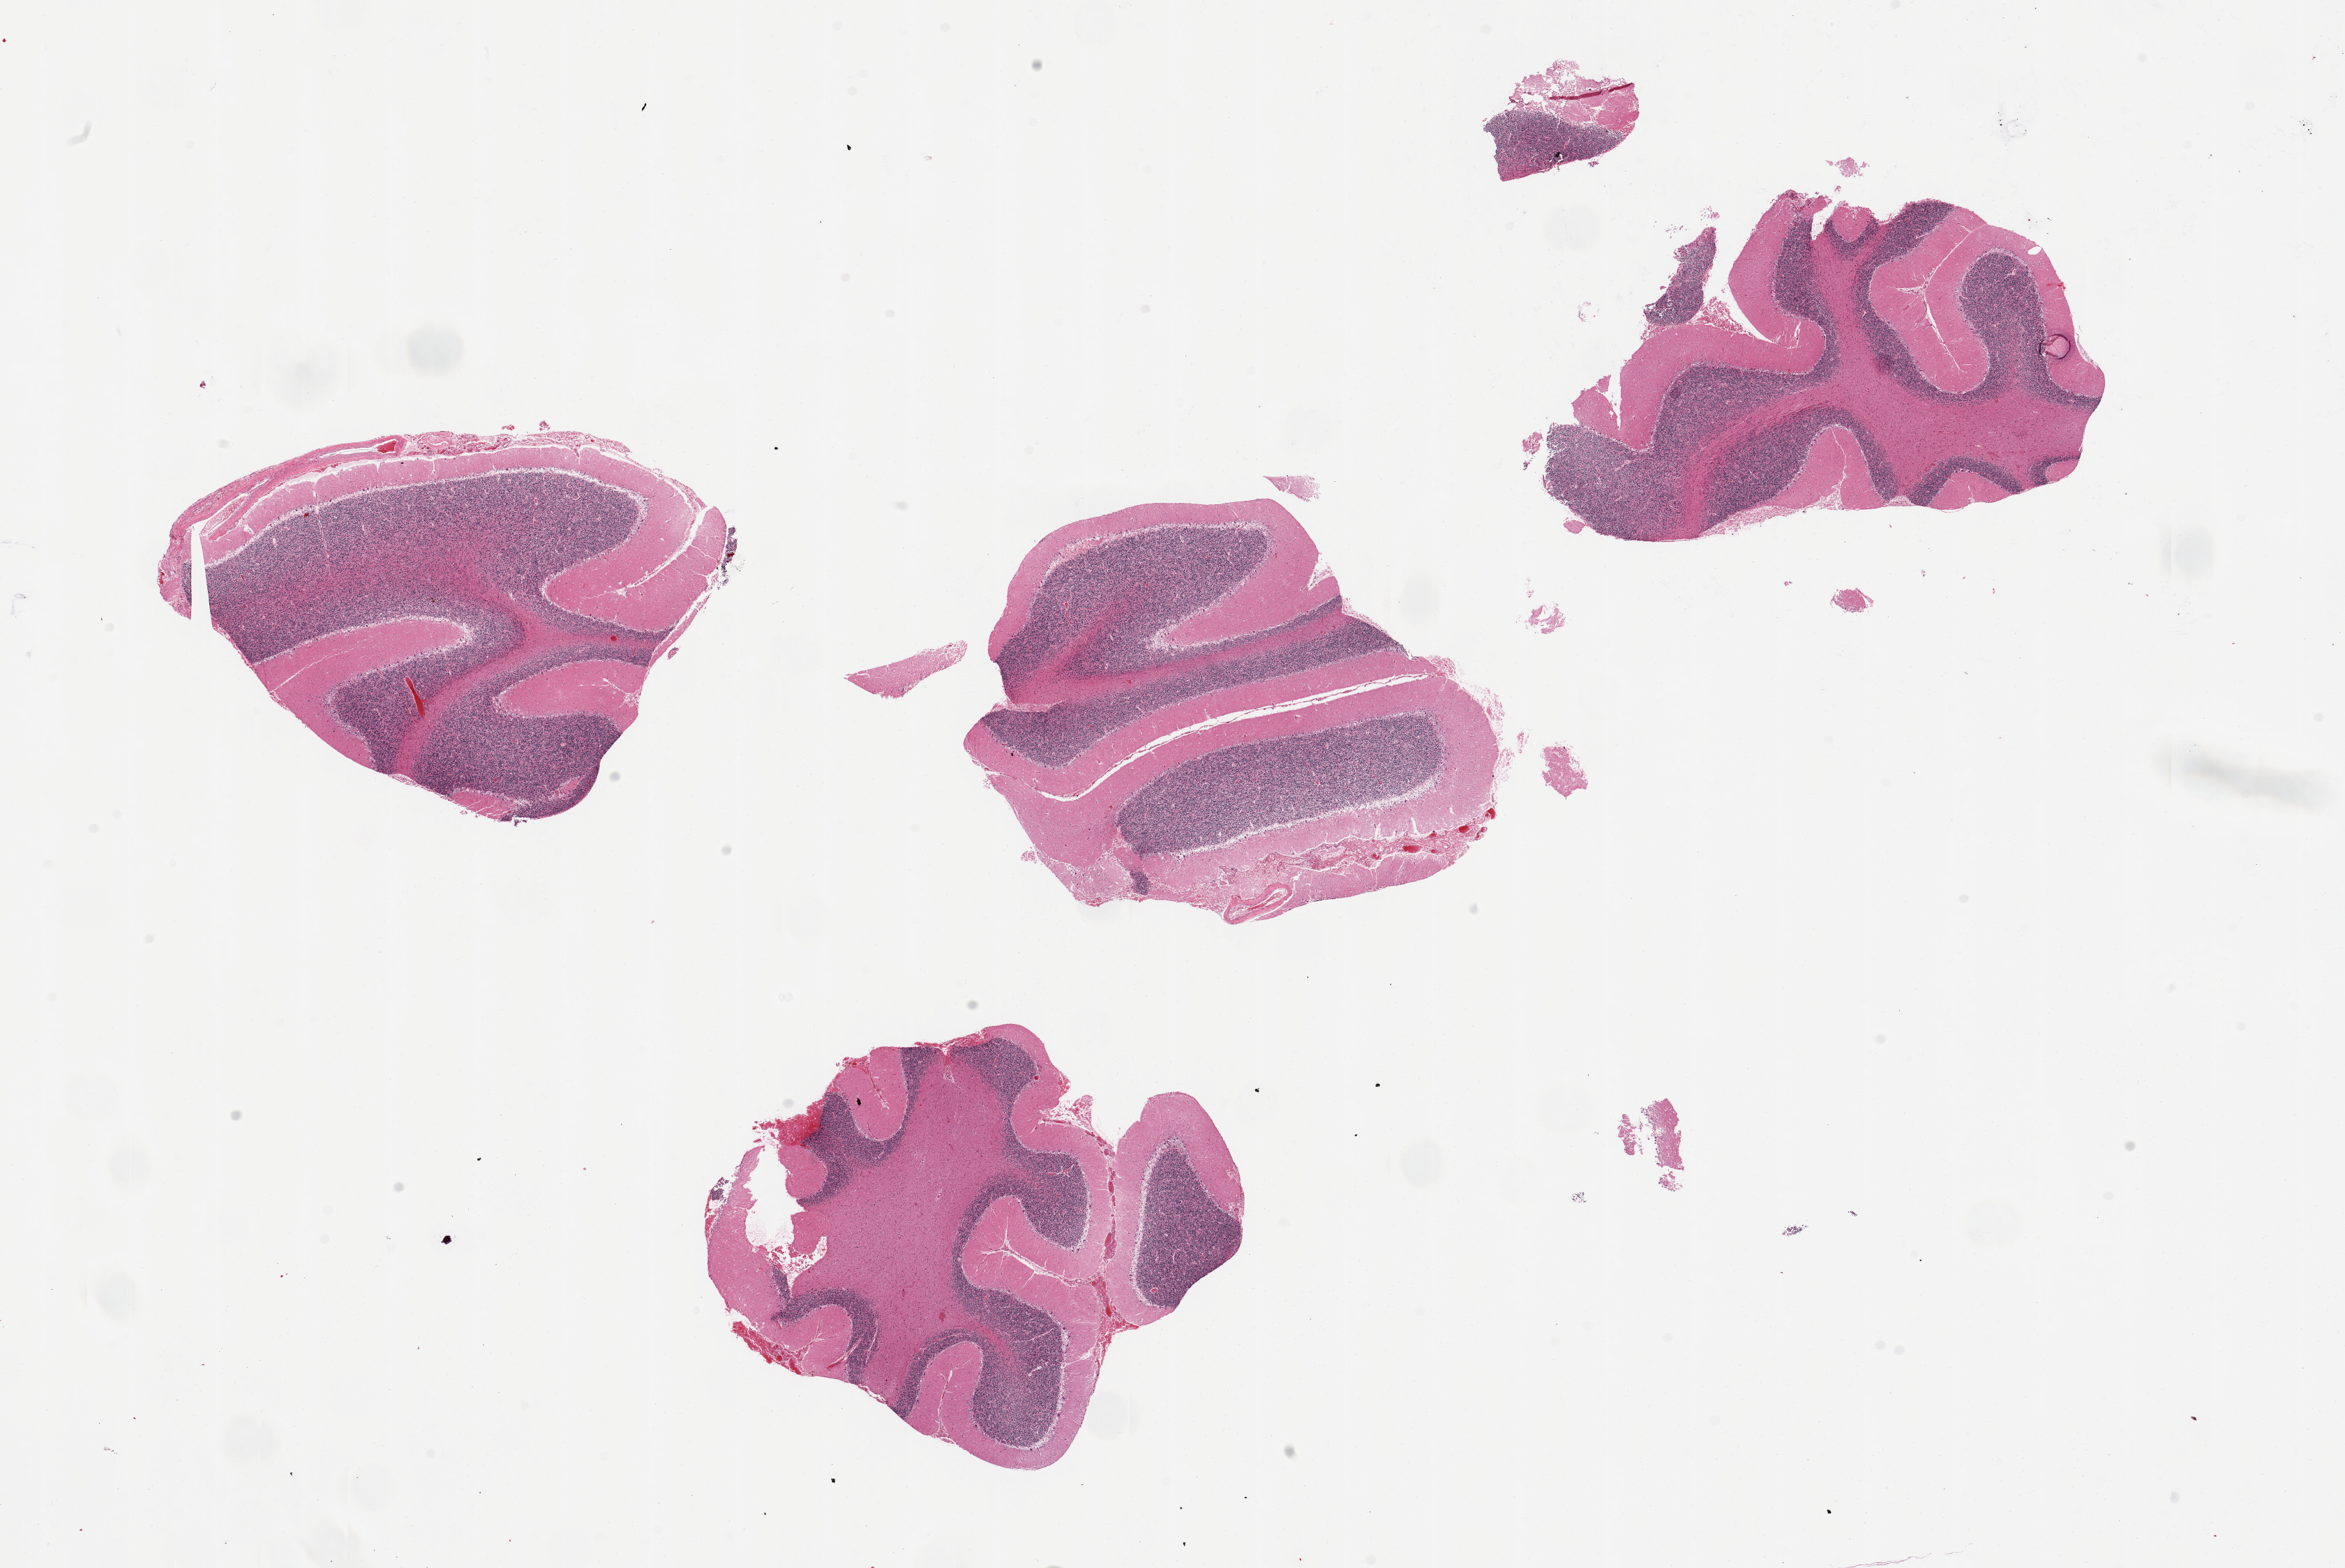
Haematoxylin and eosin whole-slide image, brightfield, low-resolution overview of the scanned area, about 26.6 x 17.8 mm (slide scanned at 20x), PAXgene-fixed, paraffin-embedded tissue, target tissue: cerebellum, tissue donor sample. Donor sex: male.
- reviewer comment on this tissue sample: 4 pieces; meningeal congestion , possible hemorrhage